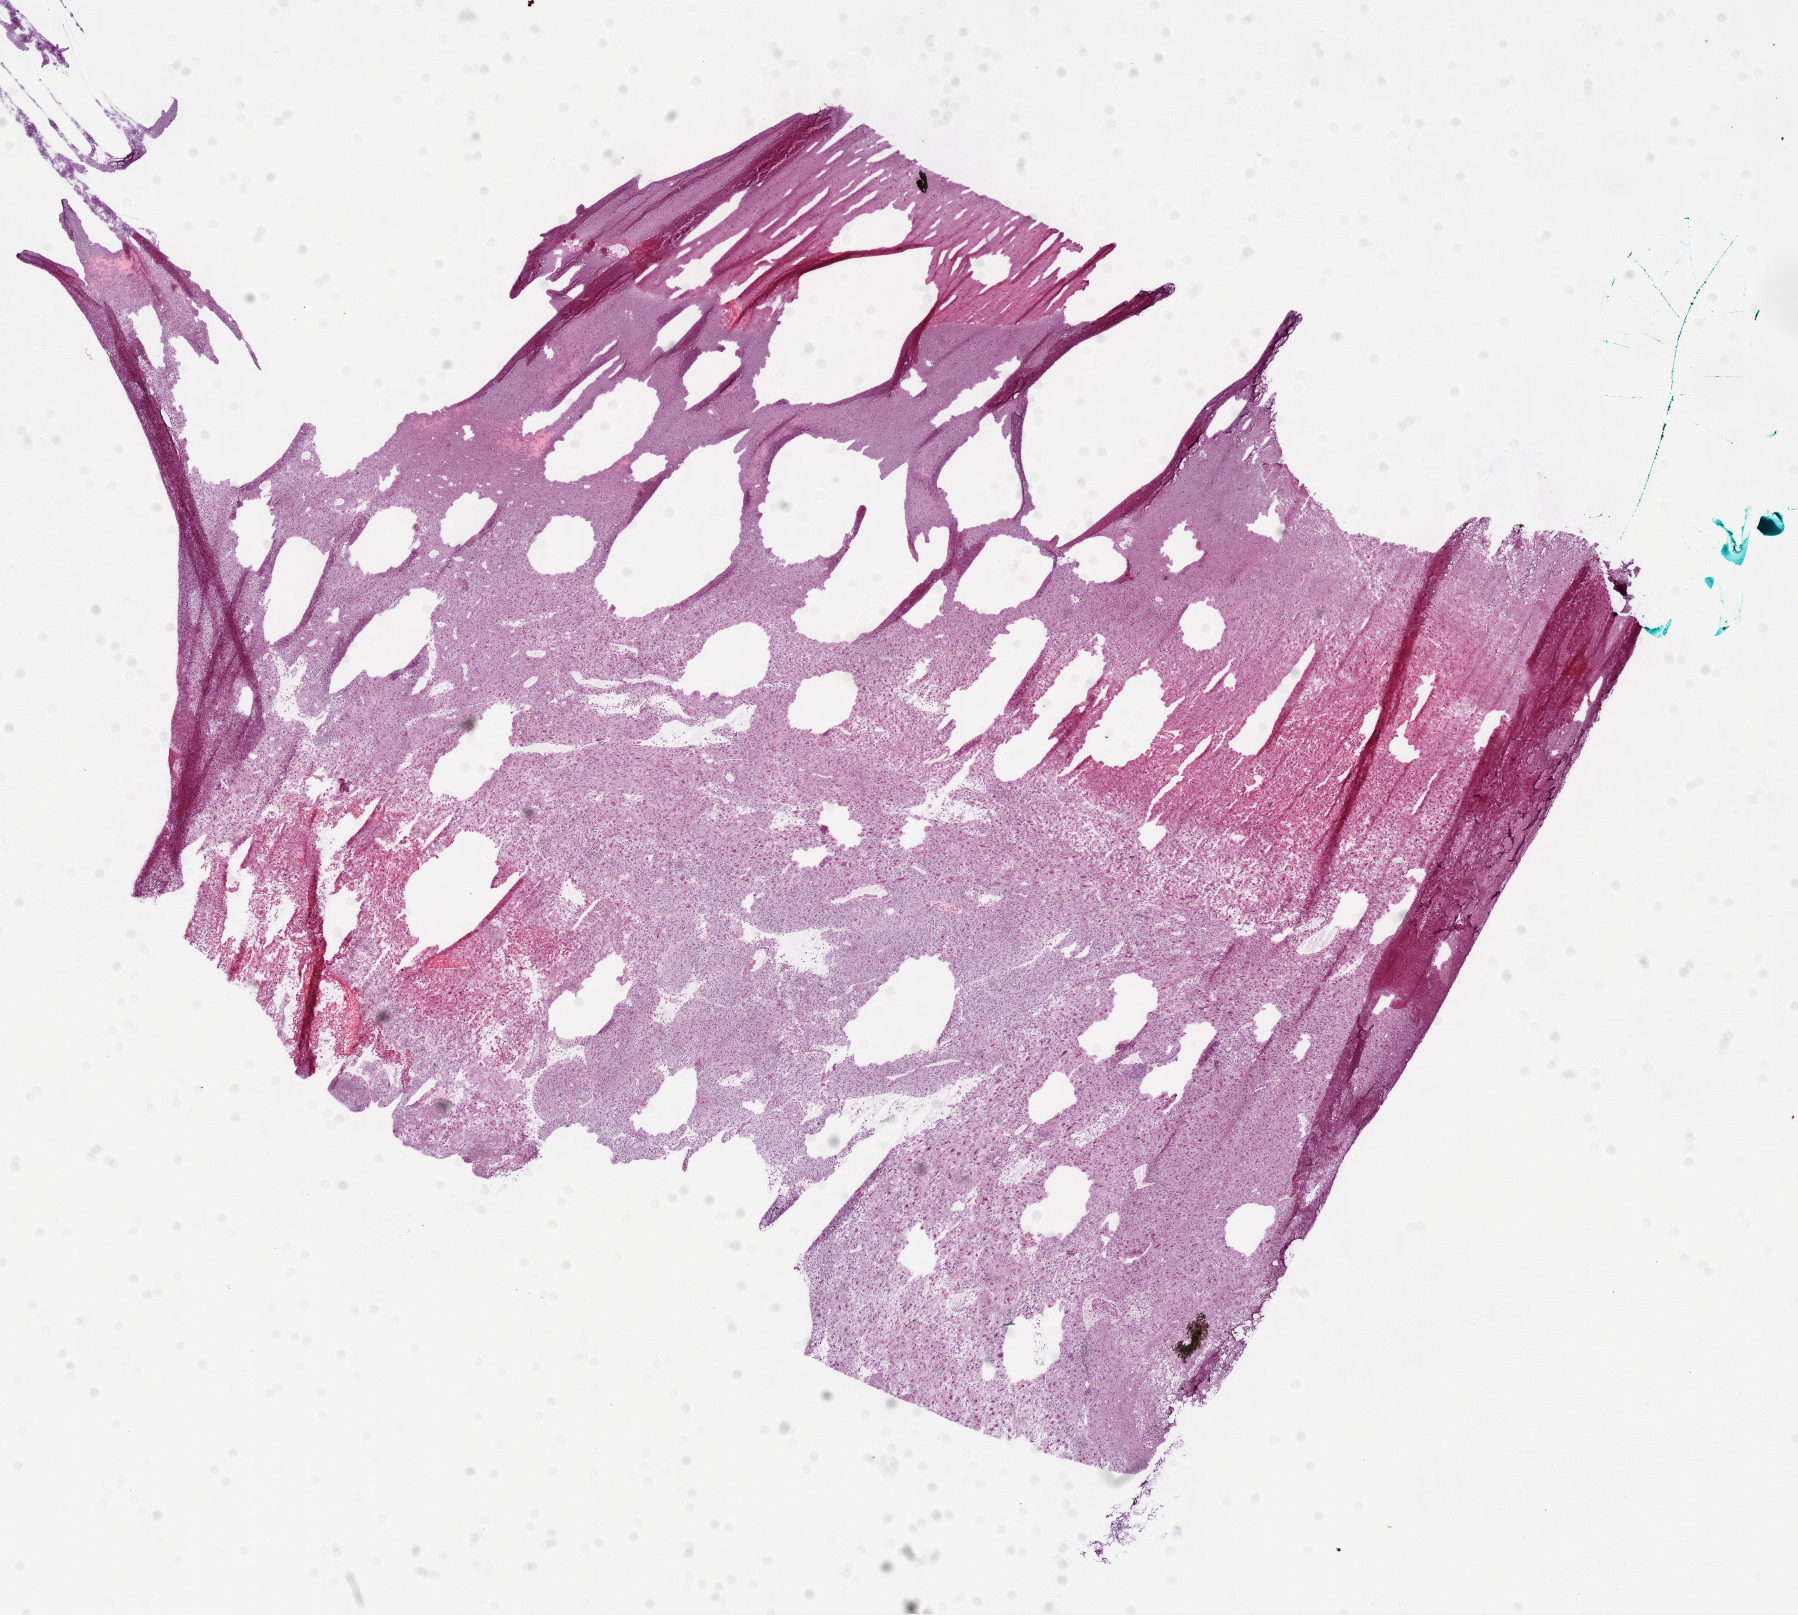
Digitized H&E tissue section (whole slide) — a low-resolution overview of the entire scanned area, about 14.5 x 13.0 mm (from a 20x scan). Frozen section. Primary tumour sample from the brain. Female, age 79 years at initial diagnosis. Composition of this section per pathologist review: tumour cells 65%, tumour nuclei 75%, normal cells 35%, stromal cells 0%, necrosis 0%.
• pathologic diagnosis: Glioblastoma